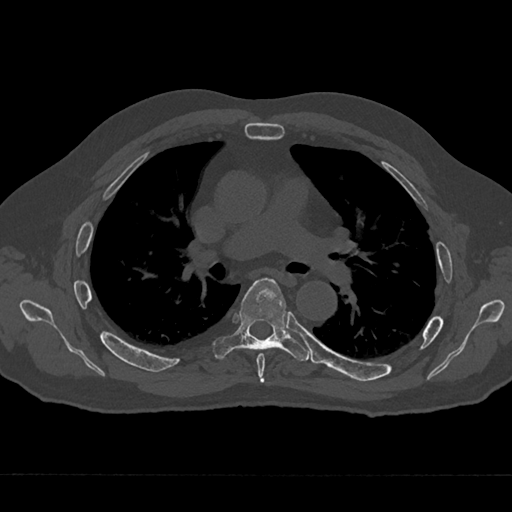
CT including the spine, one axial slice; position 437 of 797 along the scan axis; reconstruction kernel Br40s/3; bone window (W 1800 / L 400 HU); 0.5 mm slice thickness; 512 × 512 image matrix. Male patient, age 75 years. From the clinical record (not read from this slice): primary cancer: renal.
Structures marked on this image (semi-automatically segmented with operator editing):
- T5 vertebra: bounding box (x1, y1, x2, y2) in pixels: (256, 353, 265, 383)
- T6 vertebra: (213, 278, 310, 361)